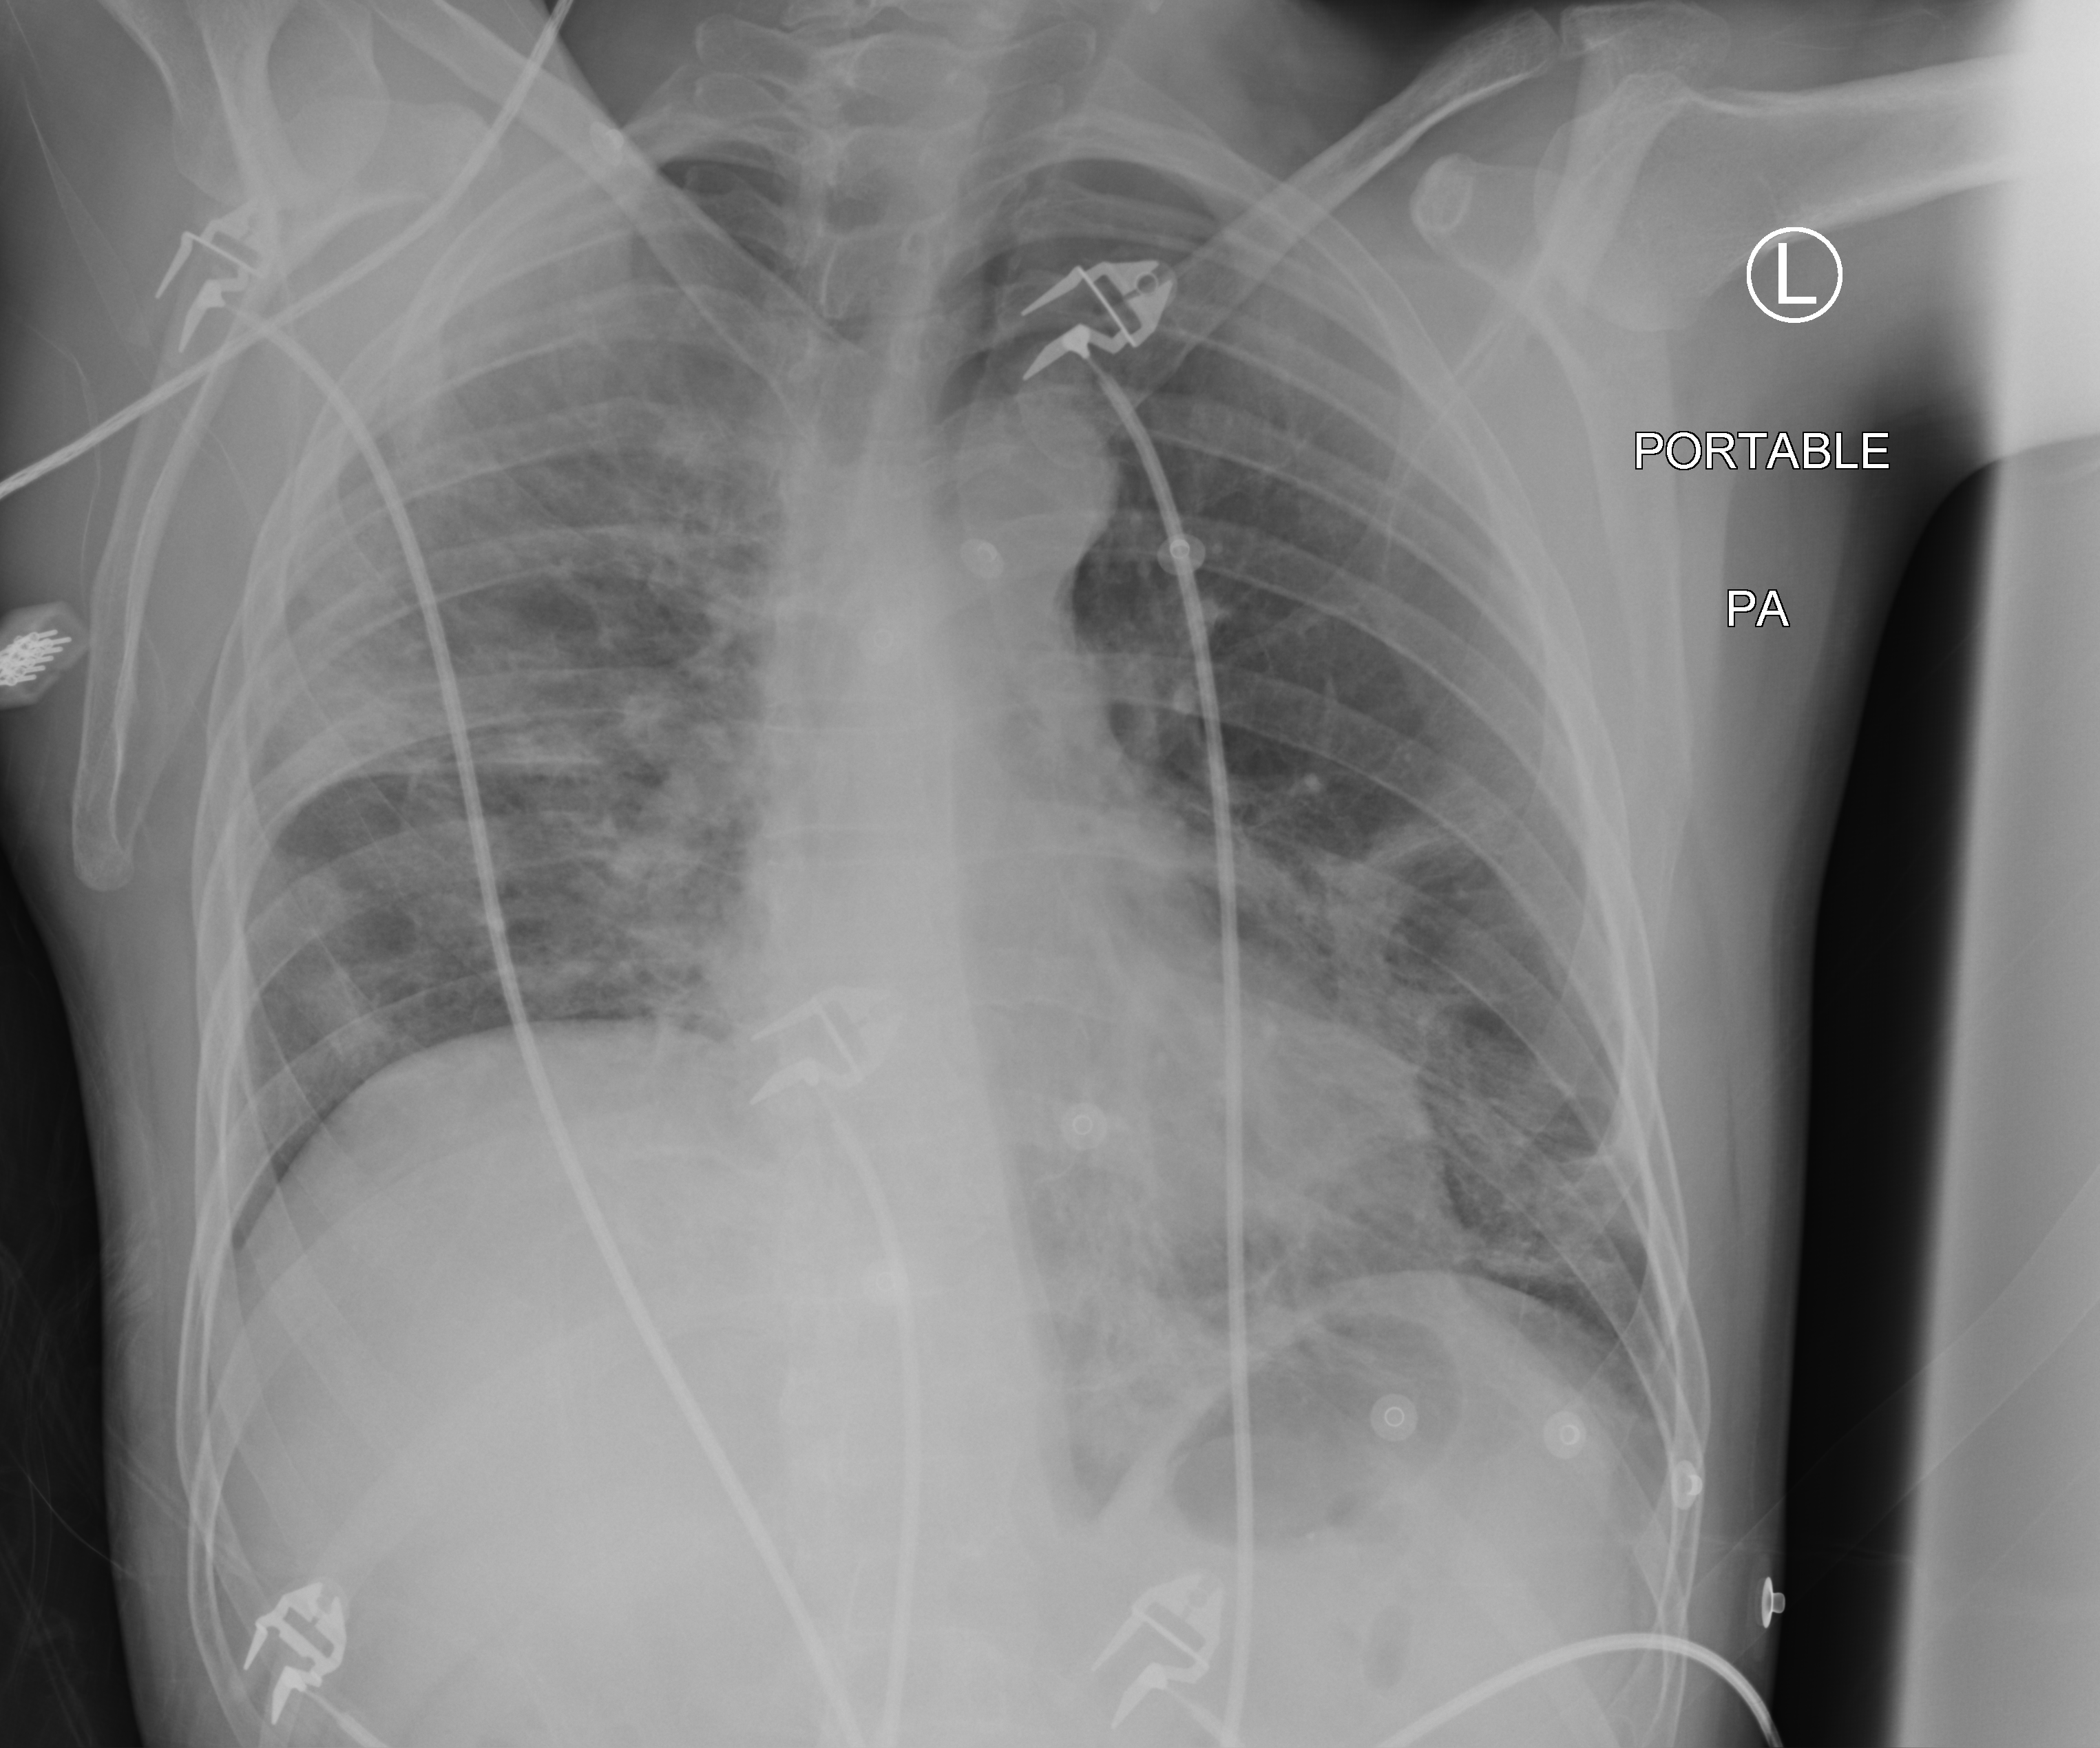
Chest radiograph (computed radiography). Patient hospitalised with COVID-19; male, aged 18–59 years.
Admission-level facts for this patient (not findings on this image; timing relative to this image not recorded): other chronic lung disease (admission record): no.